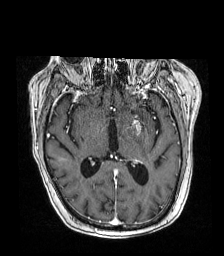
Brain MRI from a brain-tumour surgery series, one axial slice. Position 92 of 192 along the scan axis. T1-weighted post-contrast. 1 mm slice thickness. 224 × 256 image matrix. From the clinical record (not read from this slice): histopathology: Metastatic carcinoma from lung primary; tumour location: Left Frontal Caudate.
Outlined on this slice (expert manual segmentation):
- tumour: bounding box <135,116,146,131> (left, top, right, bottom; pixels)